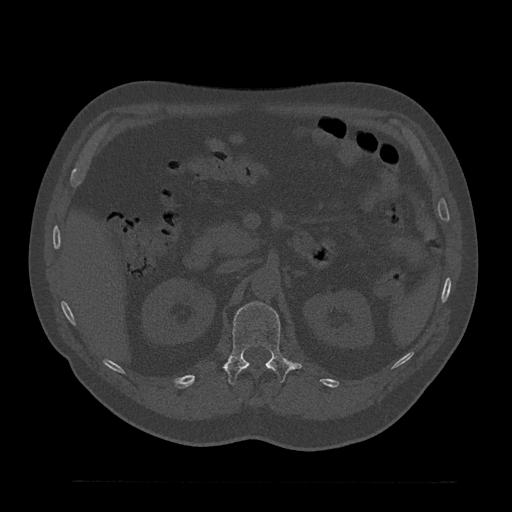
CT including the spine, one axial slice. Slice 178 of 797 in the series (ordered by position). Reconstruction kernel Br40s/3. Bone window (W 1800 / L 400 HU). 512 × 512 image matrix, field of view 430 × 430 mm. Male patient, age 61 years. From the clinical record (not read from this slice): primary cancer: prostate.
Annotated regions visible in this slice (semi-automatically segmented with operator editing):
- L1 vertebra: box from (x=224, y=302) to (x=301, y=386) px